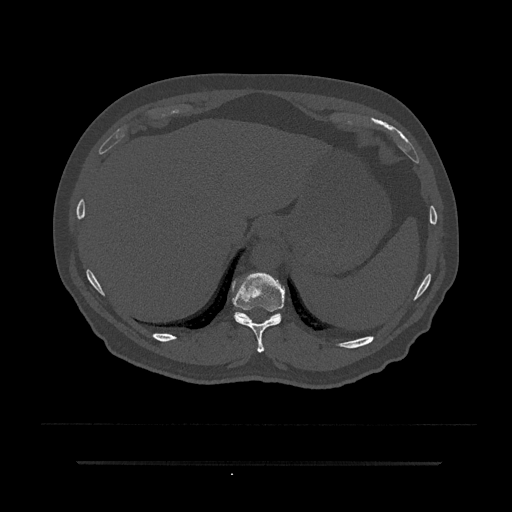
CT including the spine, one axial slice; position 310 of 797 along the scan axis; reconstruction kernel Br40s/3; bone window (W 1800 / L 400 HU); 512 × 512 image matrix. Male patient, age 59 years. Case-level facts recorded for this patient, not image findings: primary cancer: bile ducts; vertebrae with lytic lesions (as recorded): T10.
Outlined on this slice (semi-automatic segmentation, software-assisted and operator-edited):
- T10 vertebra: bounding box <232,272,285,352> (left, top, right, bottom; pixels)
- T11 vertebra: <234,312,281,321>